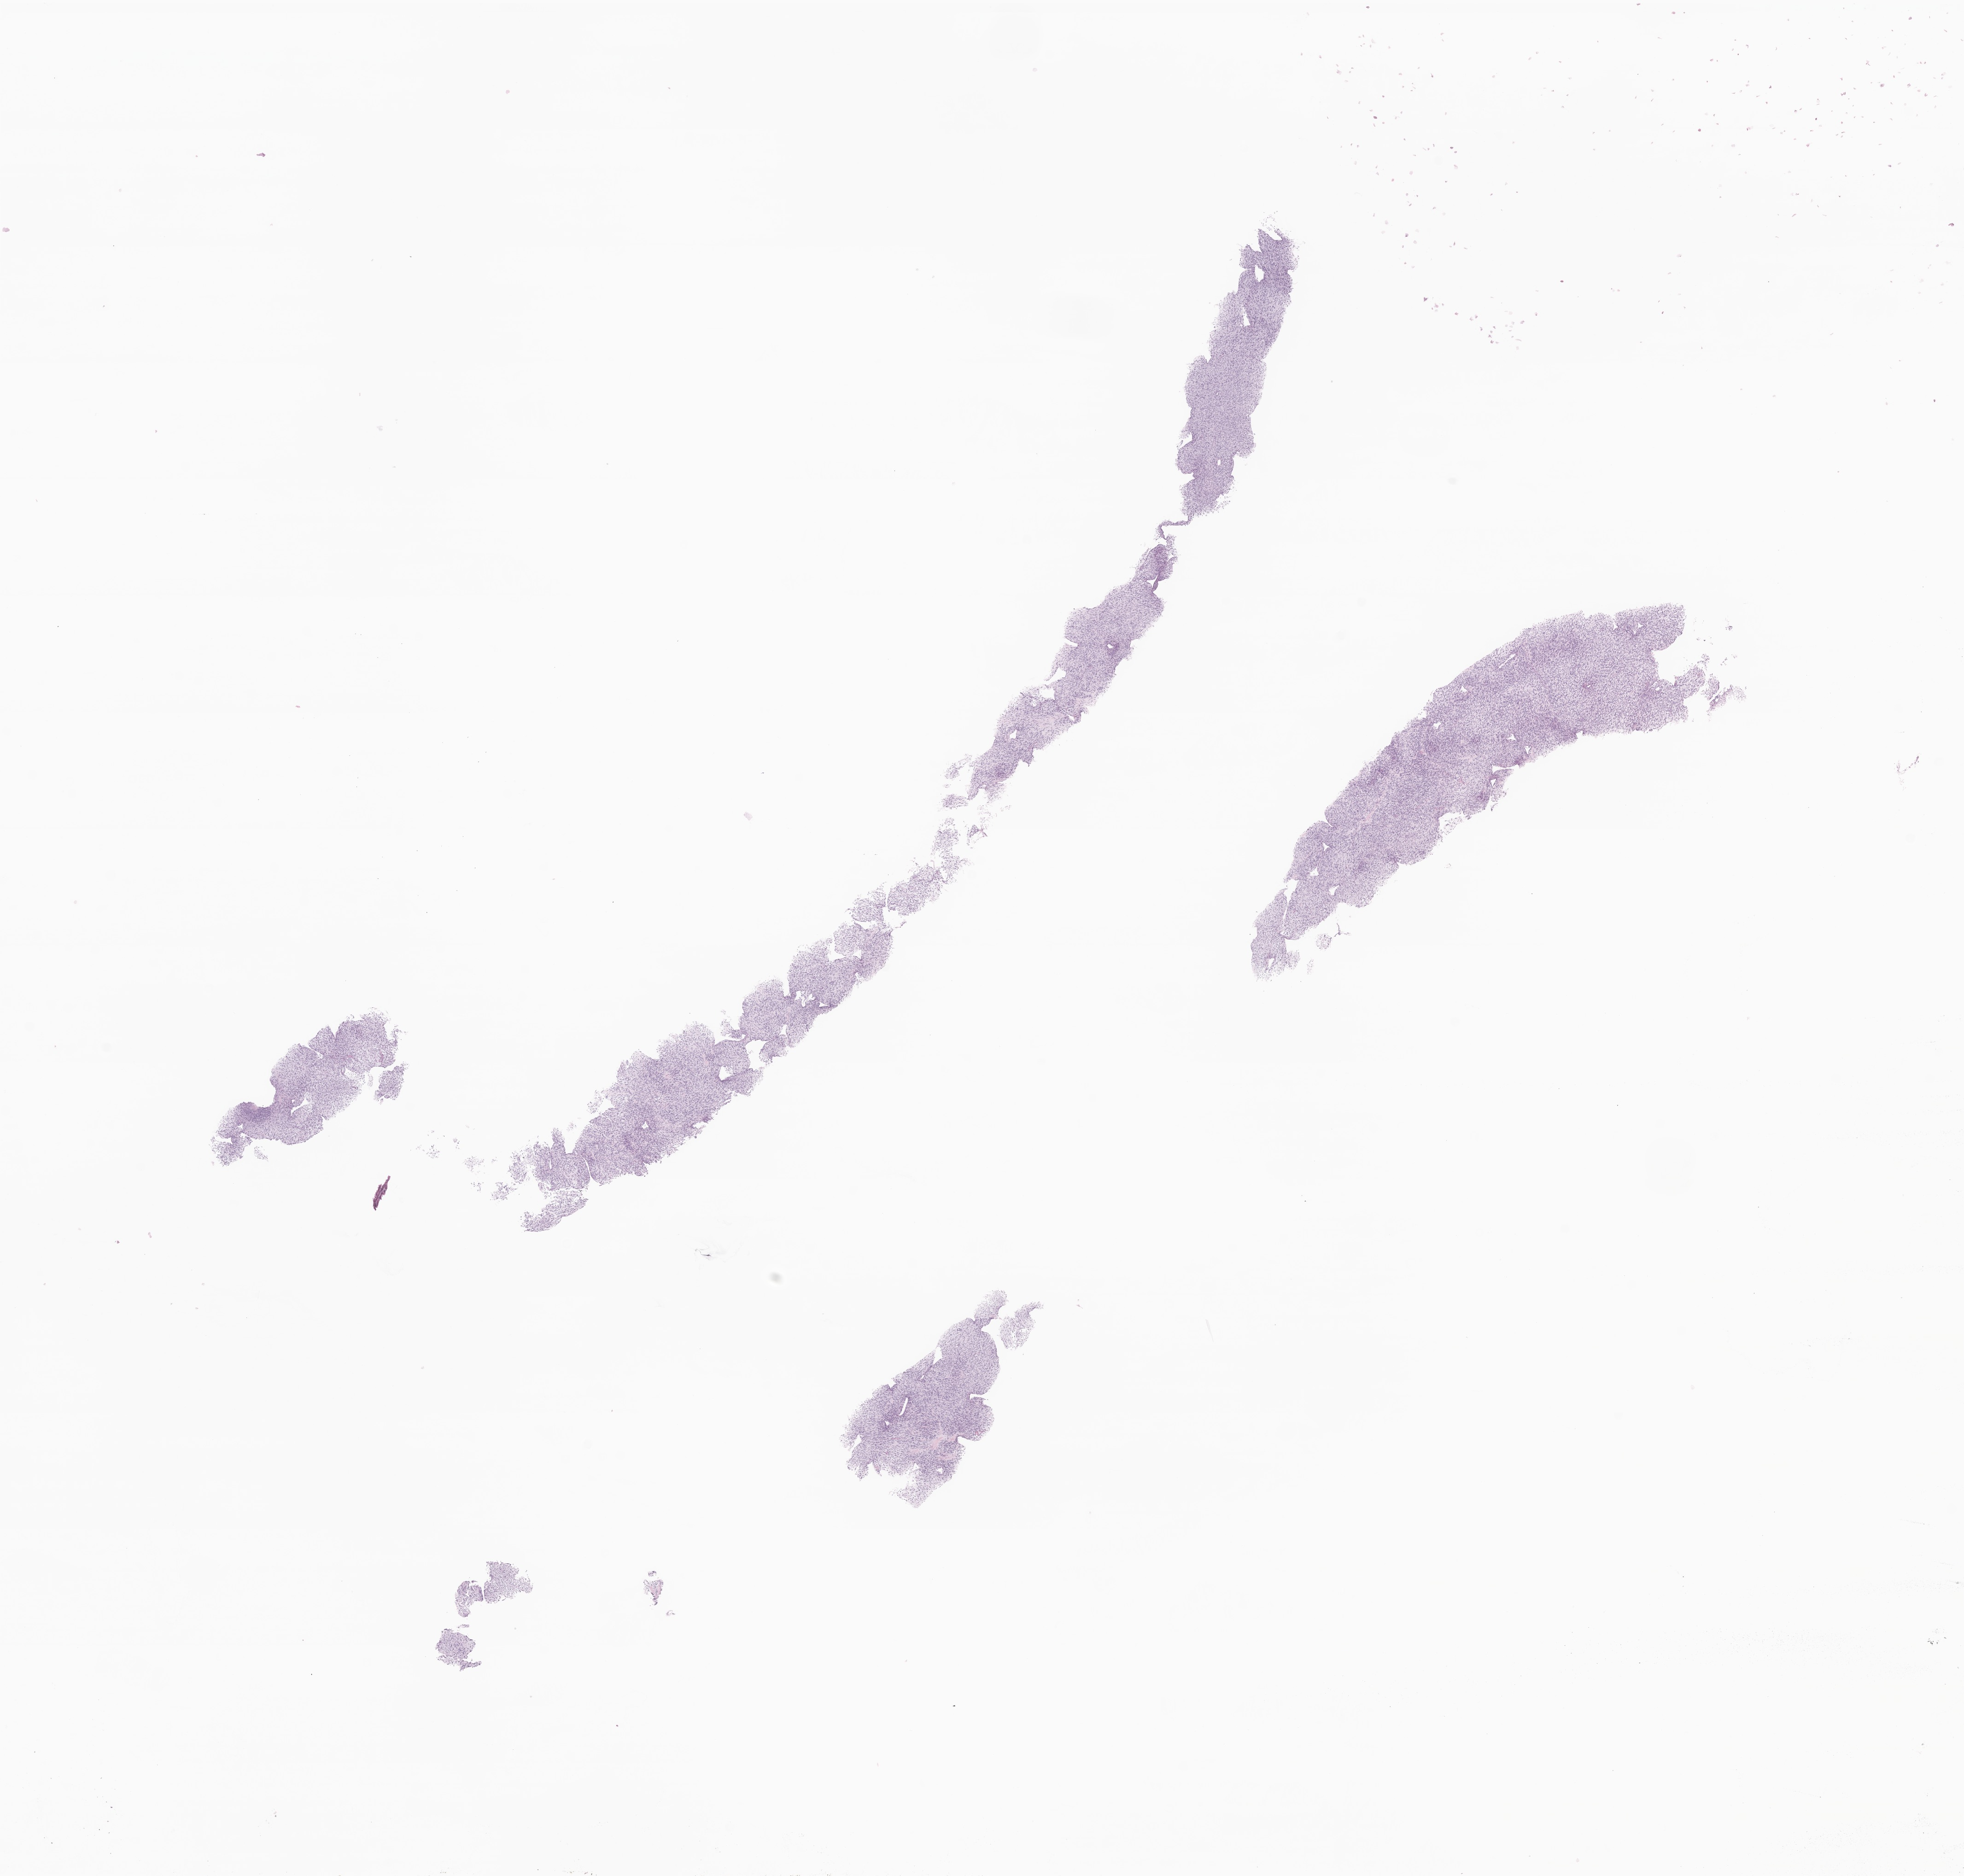
Whole-slide image, hematoxylin and eosin (H&E) stain of tumor tissue from the thorax, low-resolution overview of the scanned area, about 18.0 x 17.2 mm. FFPE section. Patient: female, age 177 months.
- diagnosis: Rhabdomyosarcoma, NOS